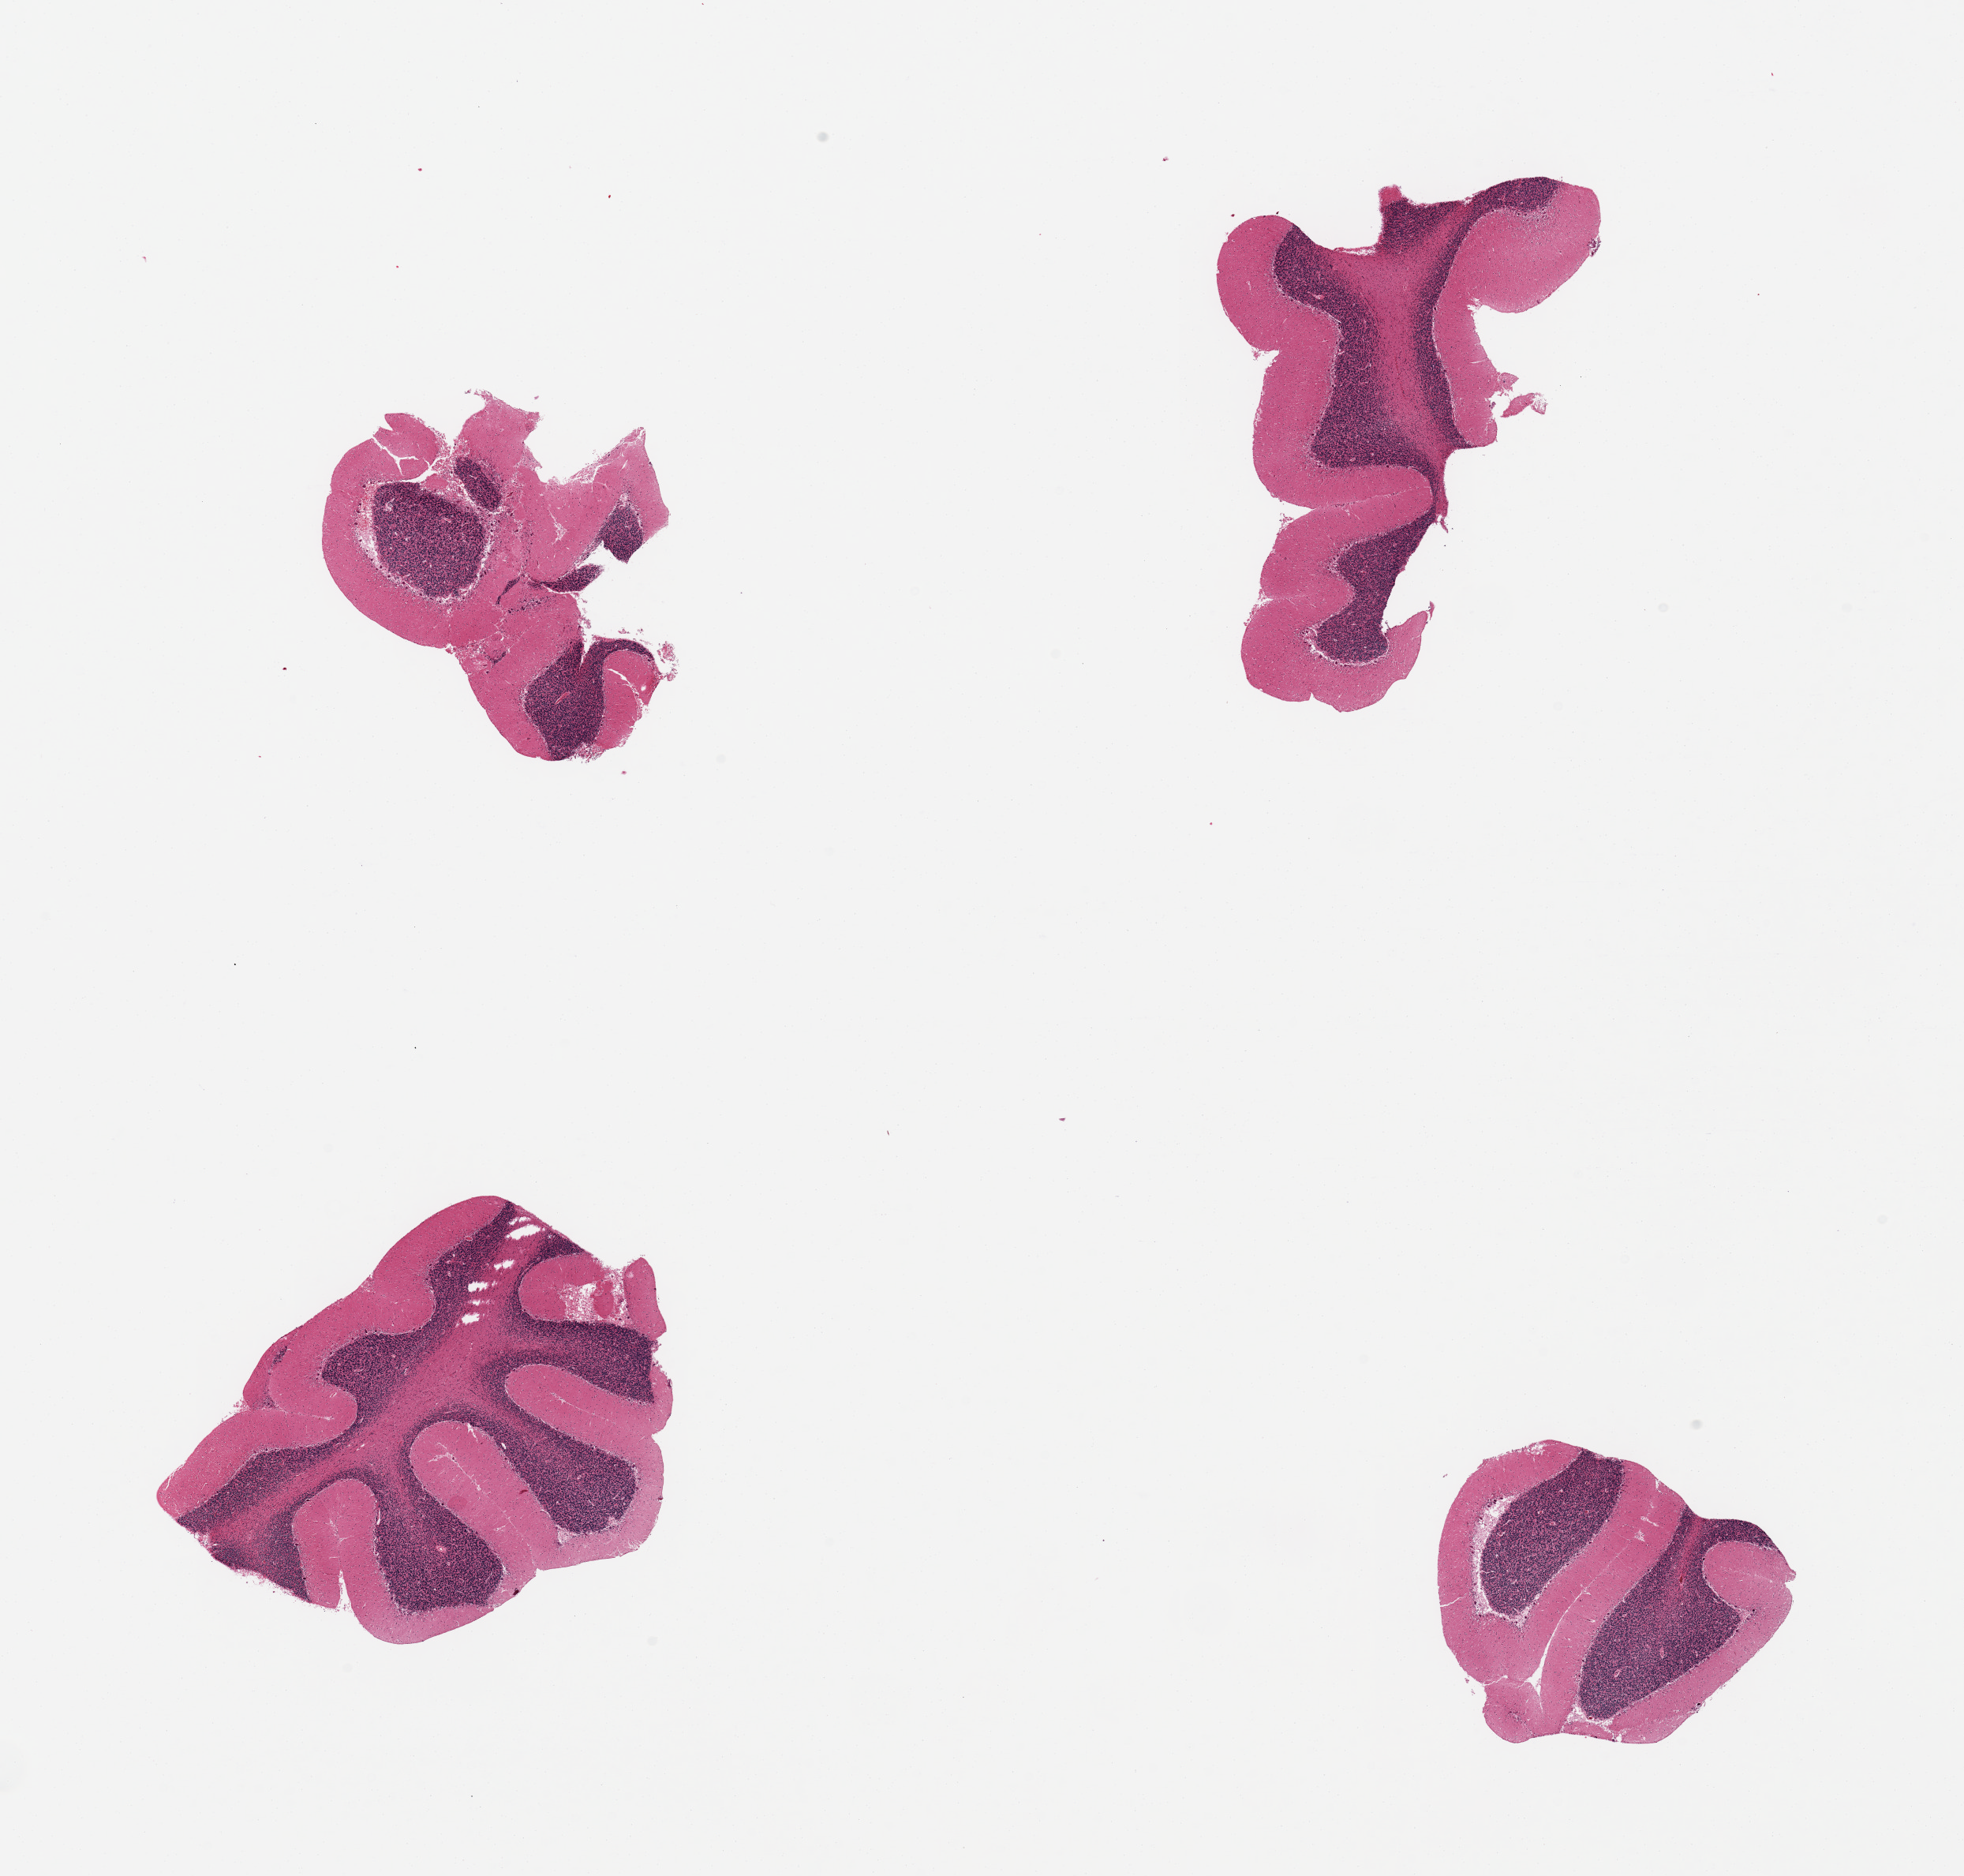
Digitized haematoxylin and eosin-stained section, brightfield — whole scanned area (about 19.7 x 18.8 mm, acquisition: 20x scan) shown as a low-resolution overview. PAXgene-fixed paraffin-embedded (PFPE) section. Sampled site (target tissue): cerebellum. Tissue donor sample. Donor sex: female.
• reviewer comment on this tissue sample: 4 pieces; Purkinje cells present